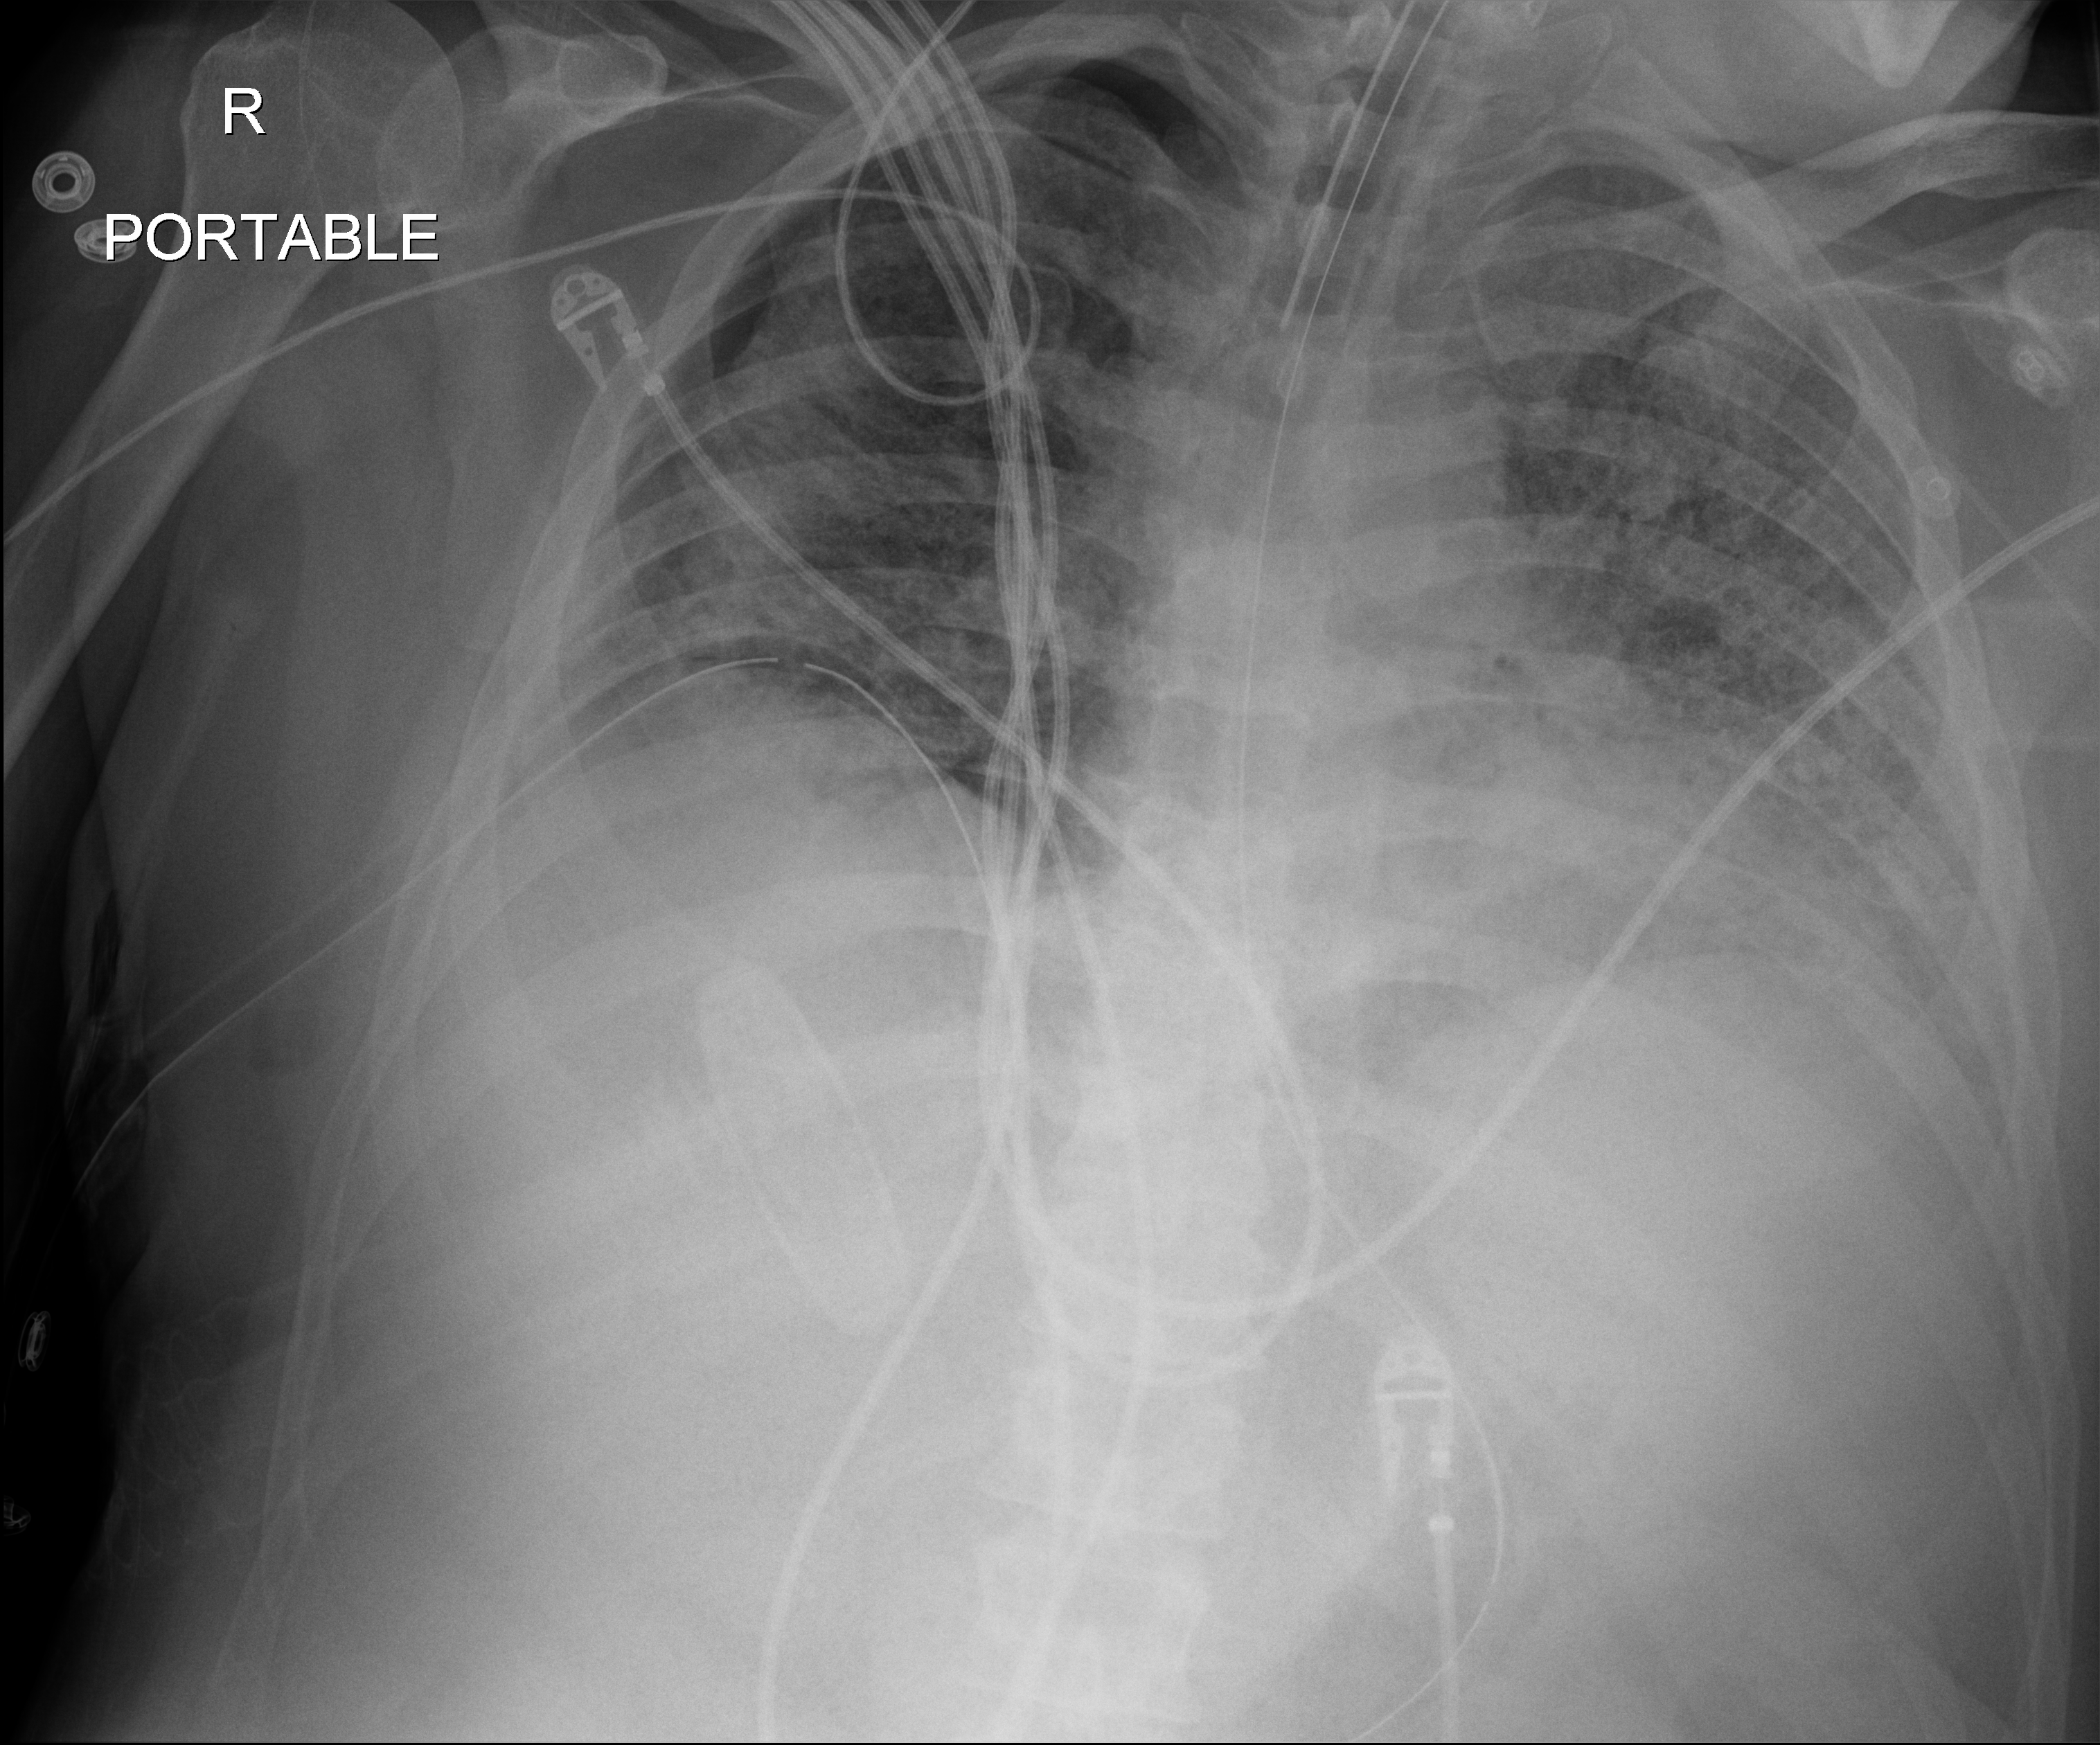
Bedside chest radiograph (digital radiography), anteroposterior (AP) projection. Male patient hospitalised with COVID-19, age 18–59 years.
Admission-level facts for this patient (not findings on this image; timing relative to this image not recorded): mechanically ventilated during this hospital stay: yes; admitted to intensive care during this hospital stay: yes.